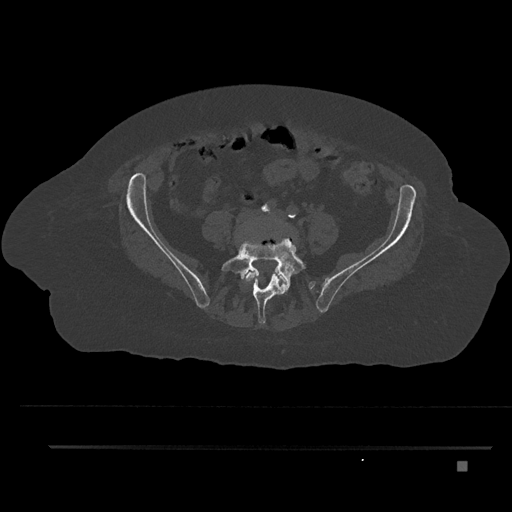
CT including the spine, one axial slice. Slice 46 of 797 in the series (ordered by position). 120 kVp. Bone window (W 1800 / L 400 HU). 512 × 512 image matrix, field of view 437 × 437 mm. Patient: female, 76 years. From the clinical record (not read from this slice): primary cancer: lung; vertebrae with lytic lesions (as recorded): T11, L3.
Outlined on this slice (semi-automatically segmented with operator editing):
- L4 vertebra: bounding box (x1, y1, x2, y2) in pixels: (244, 231, 297, 303)
- L5 vertebra: (221, 234, 307, 324)